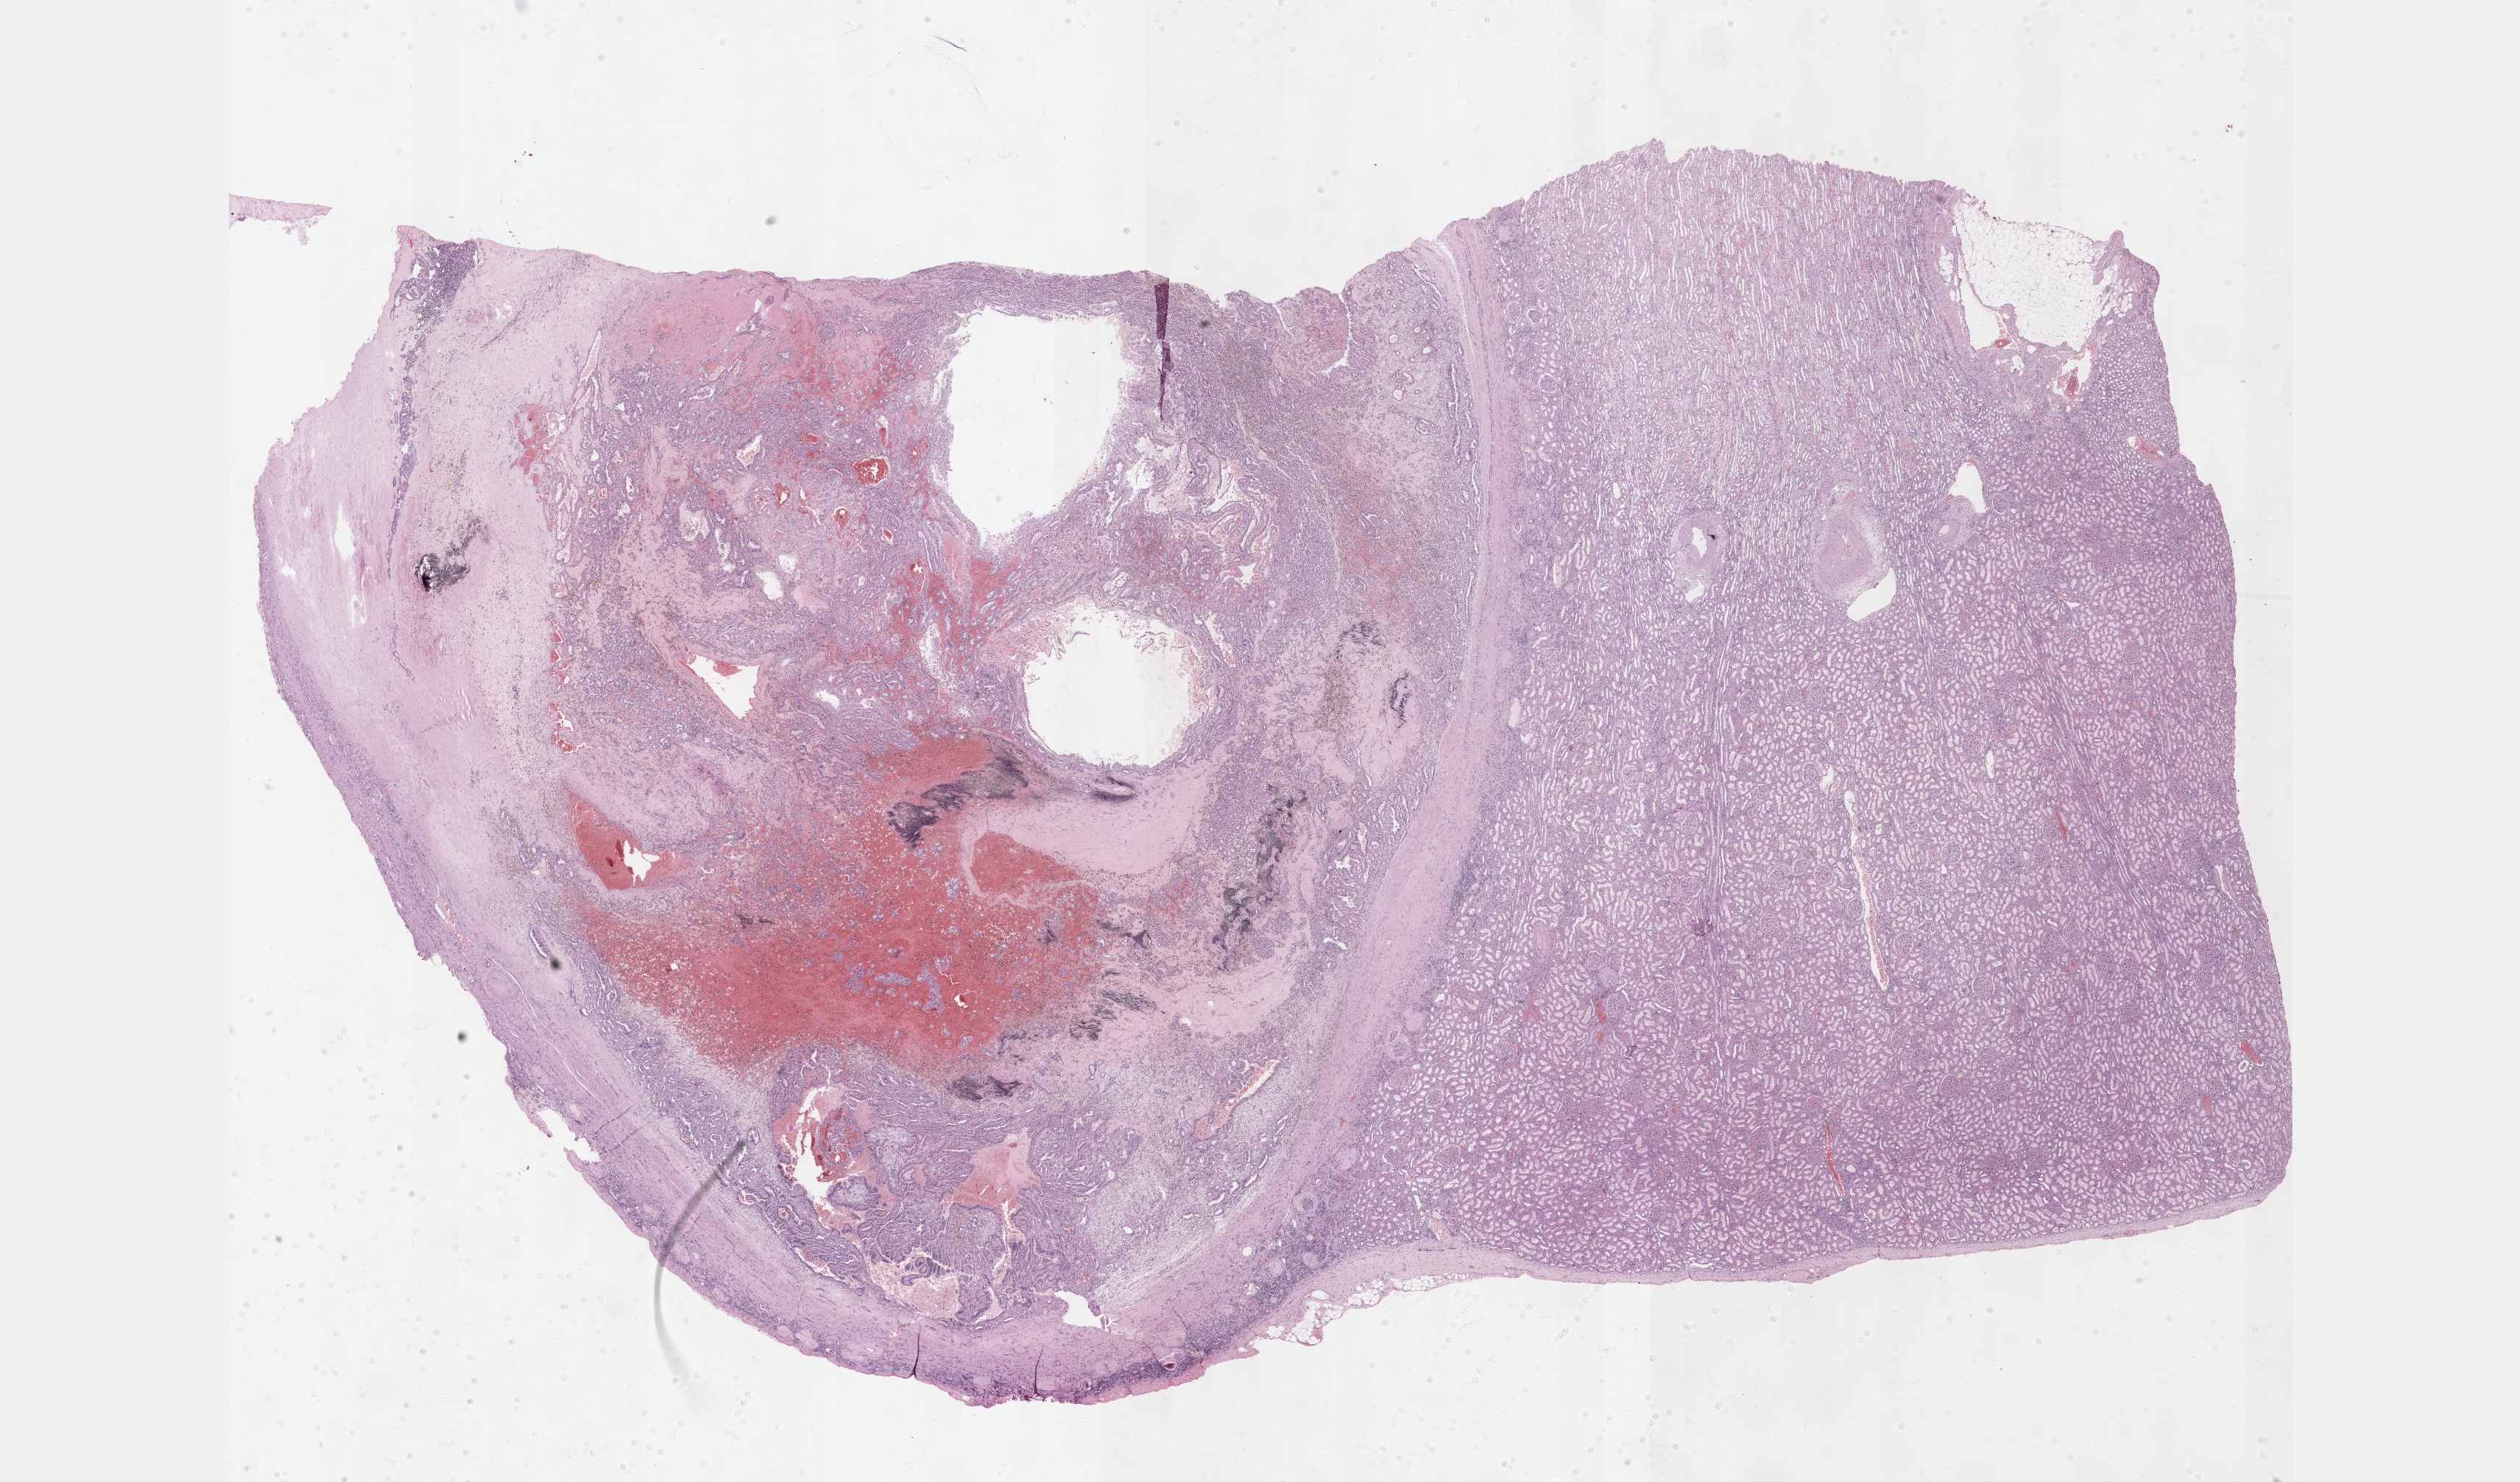
H&E whole-slide image, whole scanned area (about 27.7 x 16.3 mm) shown as a low-resolution overview, formalin-fixed paraffin-embedded (FFPE) diagnostic section, sample: primary tumour, kidney. Female patient; age at initial diagnosis 52 years.
Diagnosis: Papillary adenocarcinoma, NOS. AJCC pathologic stage: II (7th edition).